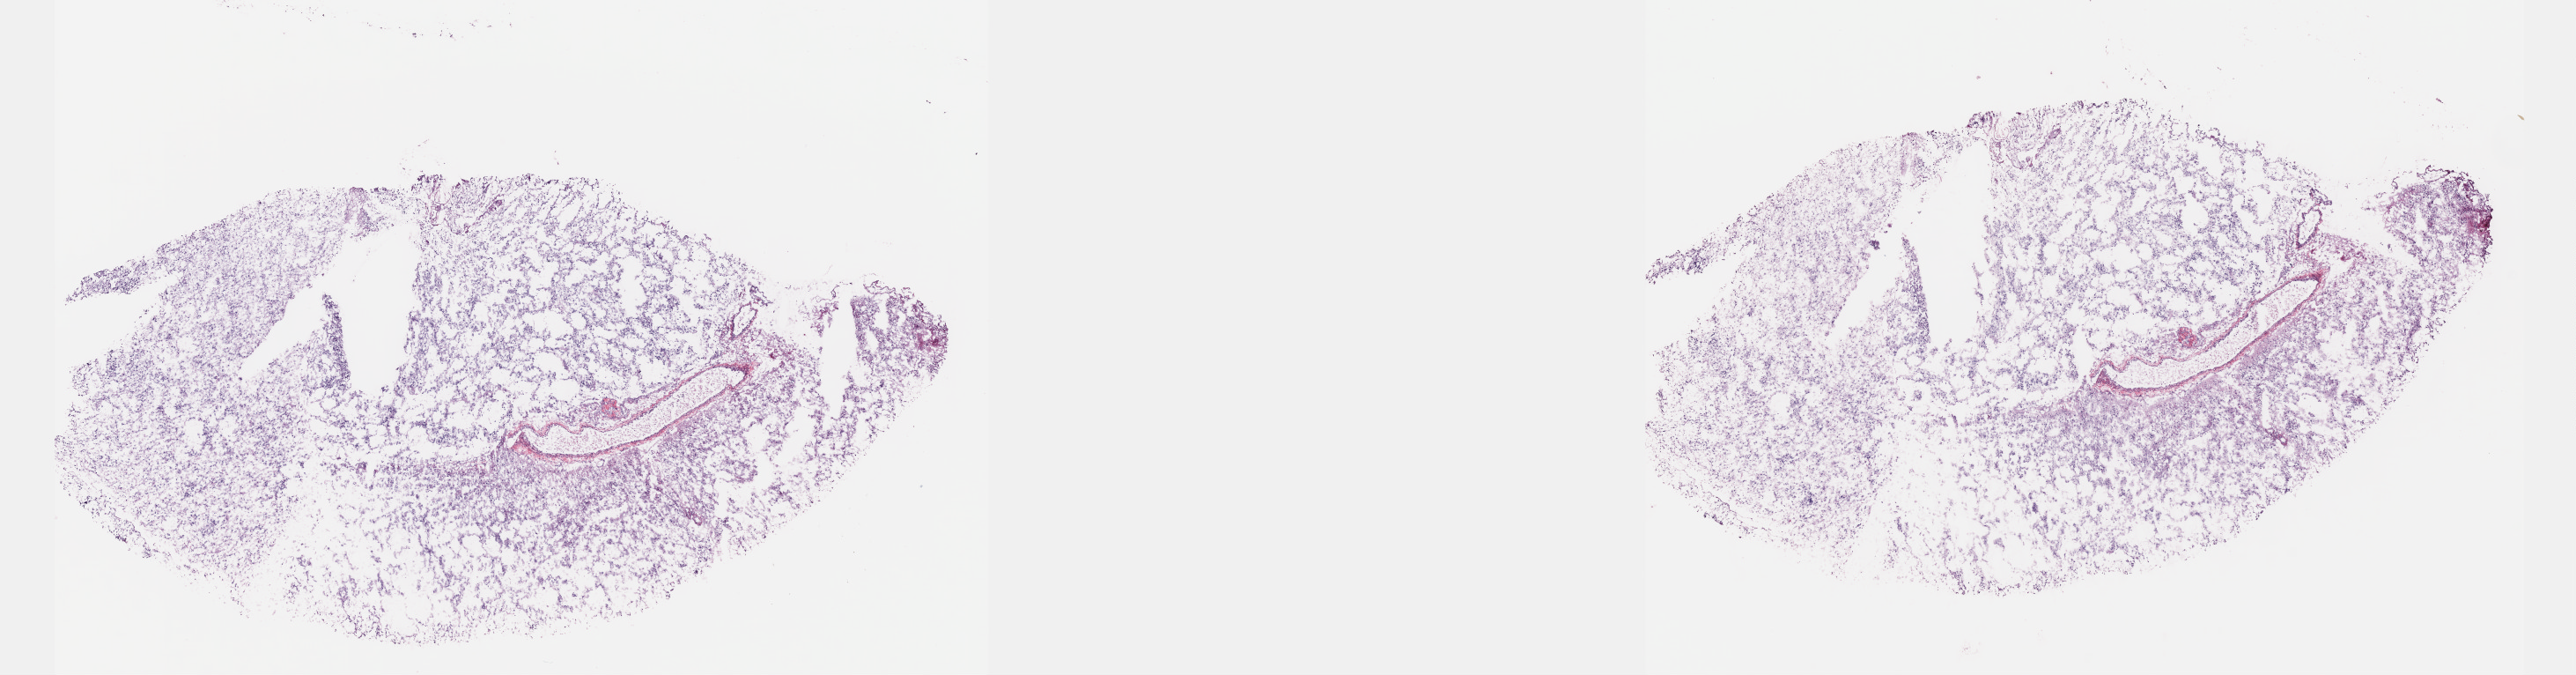
Digitized H&E-stained tissue section (whole slide), whole scanned area (about 23.6 x 6.2 mm, slide scanned at 40x) shown as a low-resolution overview, frozen section from the top of the tissue portion, sample: primary tumour, brain. Male, age 35 years at initial diagnosis. Histologic grade: G3 (poorly differentiated). Pathologist review of this section (percent, as recorded): tumour cells 50%, tumour nuclei 60%, normal cells 10%, stromal cells 40%, necrosis 0%. Infiltration values recorded for this section: lymphocyte infiltration 0%, monocyte infiltration 0%, neutrophil infiltration 0%.
- laterality: right
- diagnosis: Mixed glioma (cerebrum)